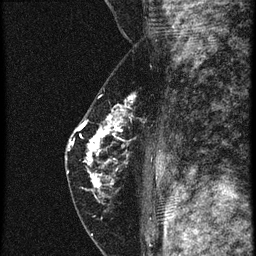
Breast MRI (dynamic contrast-enhanced), one sagittal slice. Position 36 of 60 along the scan axis. 4 images stored at this slice position (order not interpretable as contrast timing). 1.5 T. TE 4.2 ms, TR 20.4 ms. 1.5 mm slice thickness. 256 × 256 image matrix, field of view 180 × 180 mm. Female patient, age 46 years. Case-level facts recorded for this patient, not image findings: setting: breast cancer imaged before/during neoadjuvant chemotherapy; receptor status: triple-negative.
Structures marked on this image (semi-automatically segmented with operator editing):
- analysis volume of interest (the breast-tissue region the enhancement analysis was run in; not a lesion): bounding box [x1, y1, x2, y2] px = [67, 94, 153, 201]
- tumour enhancement mask (voxels above the 90 % enhancement threshold inside the analysis volume of interest): [70, 110, 126, 187]